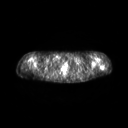
FDG PET of an extremity soft-tissue mass (from a PET/CT study), one axial slice. 128 × 128 image matrix. Patient: female, 28 years. Case-level facts recorded for this patient, not image findings: histological type: malignant fibrous histiocytoma; grade: low; site of the primary tumour: left arm.
Annotated regions visible in this slice (expert contour drawn on MRI and transferred to this co-registered scan by the dataset authors):
- gross tumour volume (mass): bounding box (x1, y1, x2, y2) in pixels: (100, 65, 105, 69)